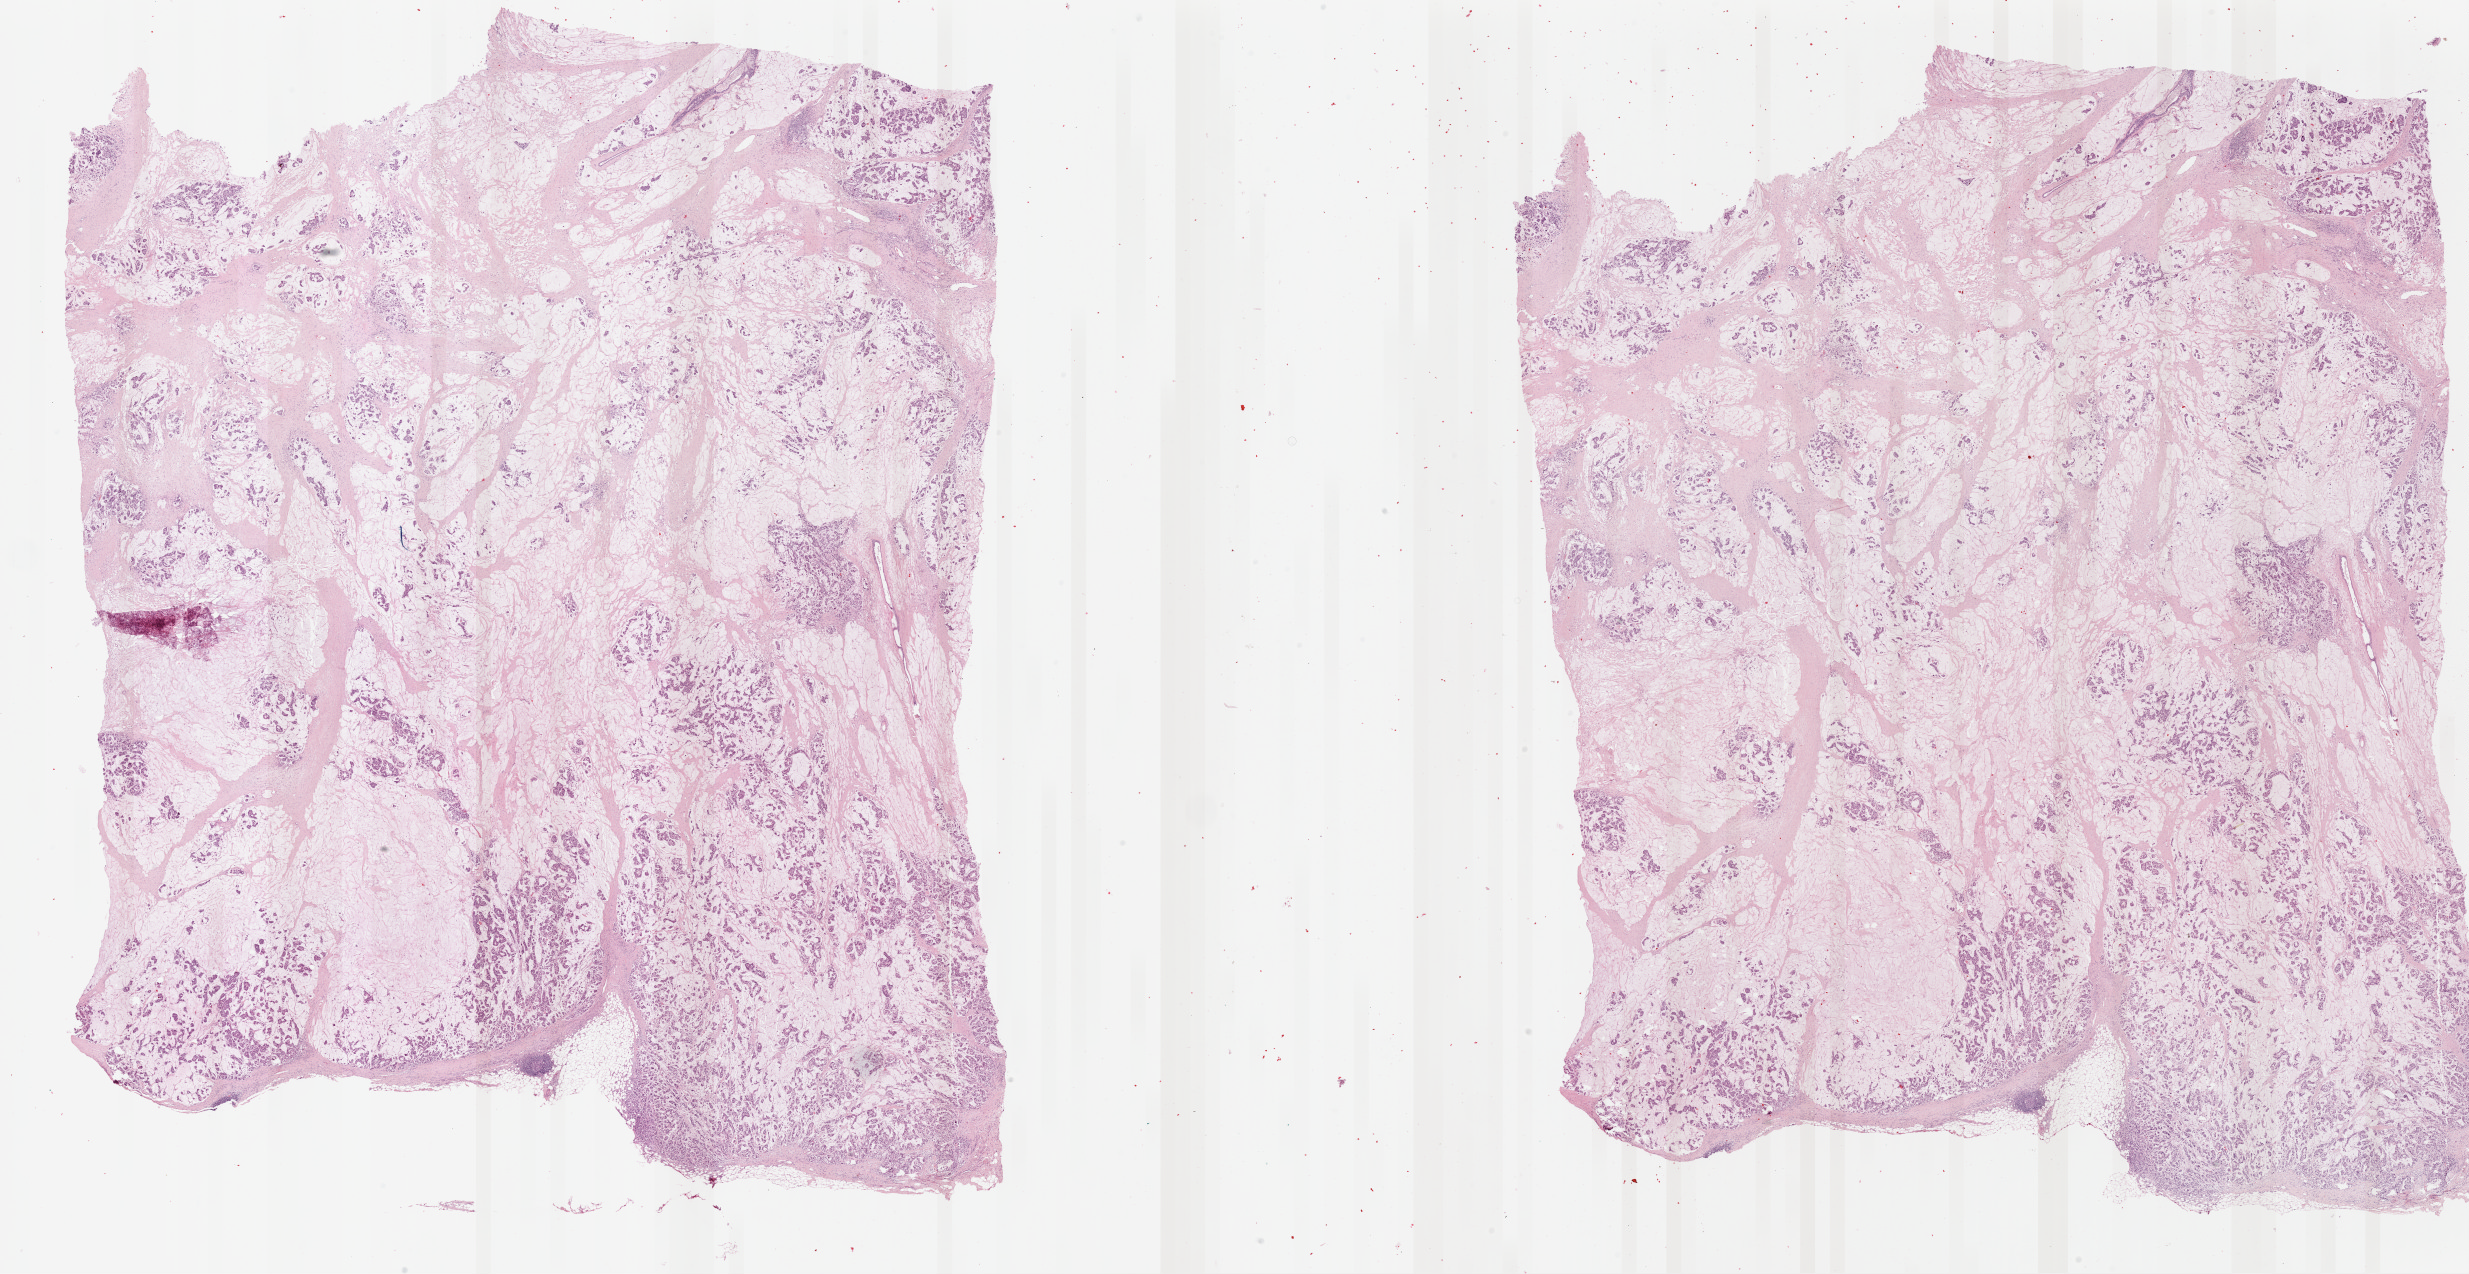
Digitized H&E tissue section (whole slide) — whole scanned area (about 39.0 x 20.1 mm, from a 40x scan) shown as a low-resolution overview. Formalin-fixed paraffin-embedded (FFPE) diagnostic section. Breast, primary tumour sample. Female patient; age at initial diagnosis 55 years.
- diagnosis: Mucinous adenocarcinoma
- lymph nodes positive (case pathology): 0 of 12 examined
- laterality: right
- AJCC pathologic stage: IIIB (7th edition)